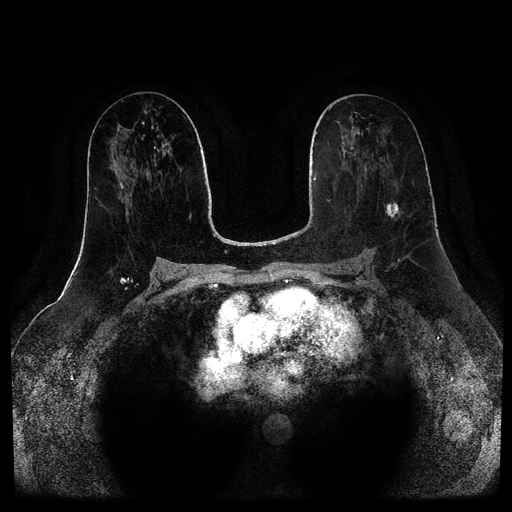
Breast MRI (dynamic contrast-enhanced, multi-phase), one axial slice; position 44 of 116 along the scan axis; dynamic contrast-enhanced series, time point 2 of 5 at this slice position (early post-contrast); 1.5 T; TE 2.6 ms, TR 5.2 ms; 512 × 512 image matrix, field of view 380 × 380 mm. Female patient, age 57 years.
Structures marked on this image (semi-automatically segmented with operator editing):
- breast lesion (labelled 'tumour' in the annotation; benign lesions carry a separate 'benign' label): box from (x=386, y=203) to (x=399, y=218) px